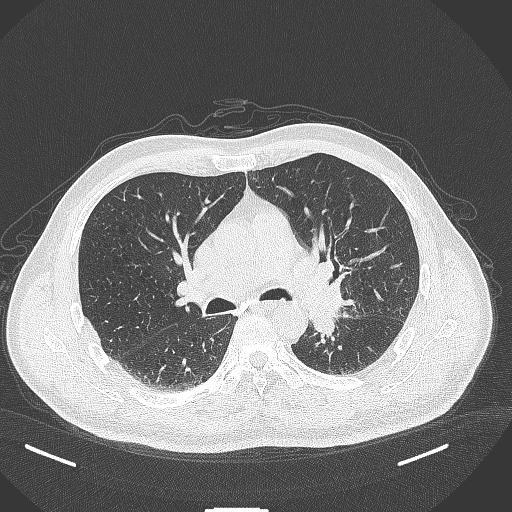
Chest CT, one axial slice; position 250 of 429 along the scan axis; reconstruction kernel B70f; 120 kVp; lung window (W 1500 / L -600 HU); 1 mm slice thickness; 512 × 512 image matrix, field of view 400 × 400 mm. Patient: male, 55 years. Case-level facts recorded for this patient, not image findings: clinical TNM (as recorded): T3 N0 M1c; histopathological grade: G3.
Structures marked on this image (rectangle marked by the reading radiologist):
- lung tumour (recorded histology: adenocarcinoma): bounding box (x1, y1, x2, y2) in pixels: (305, 296, 344, 342)